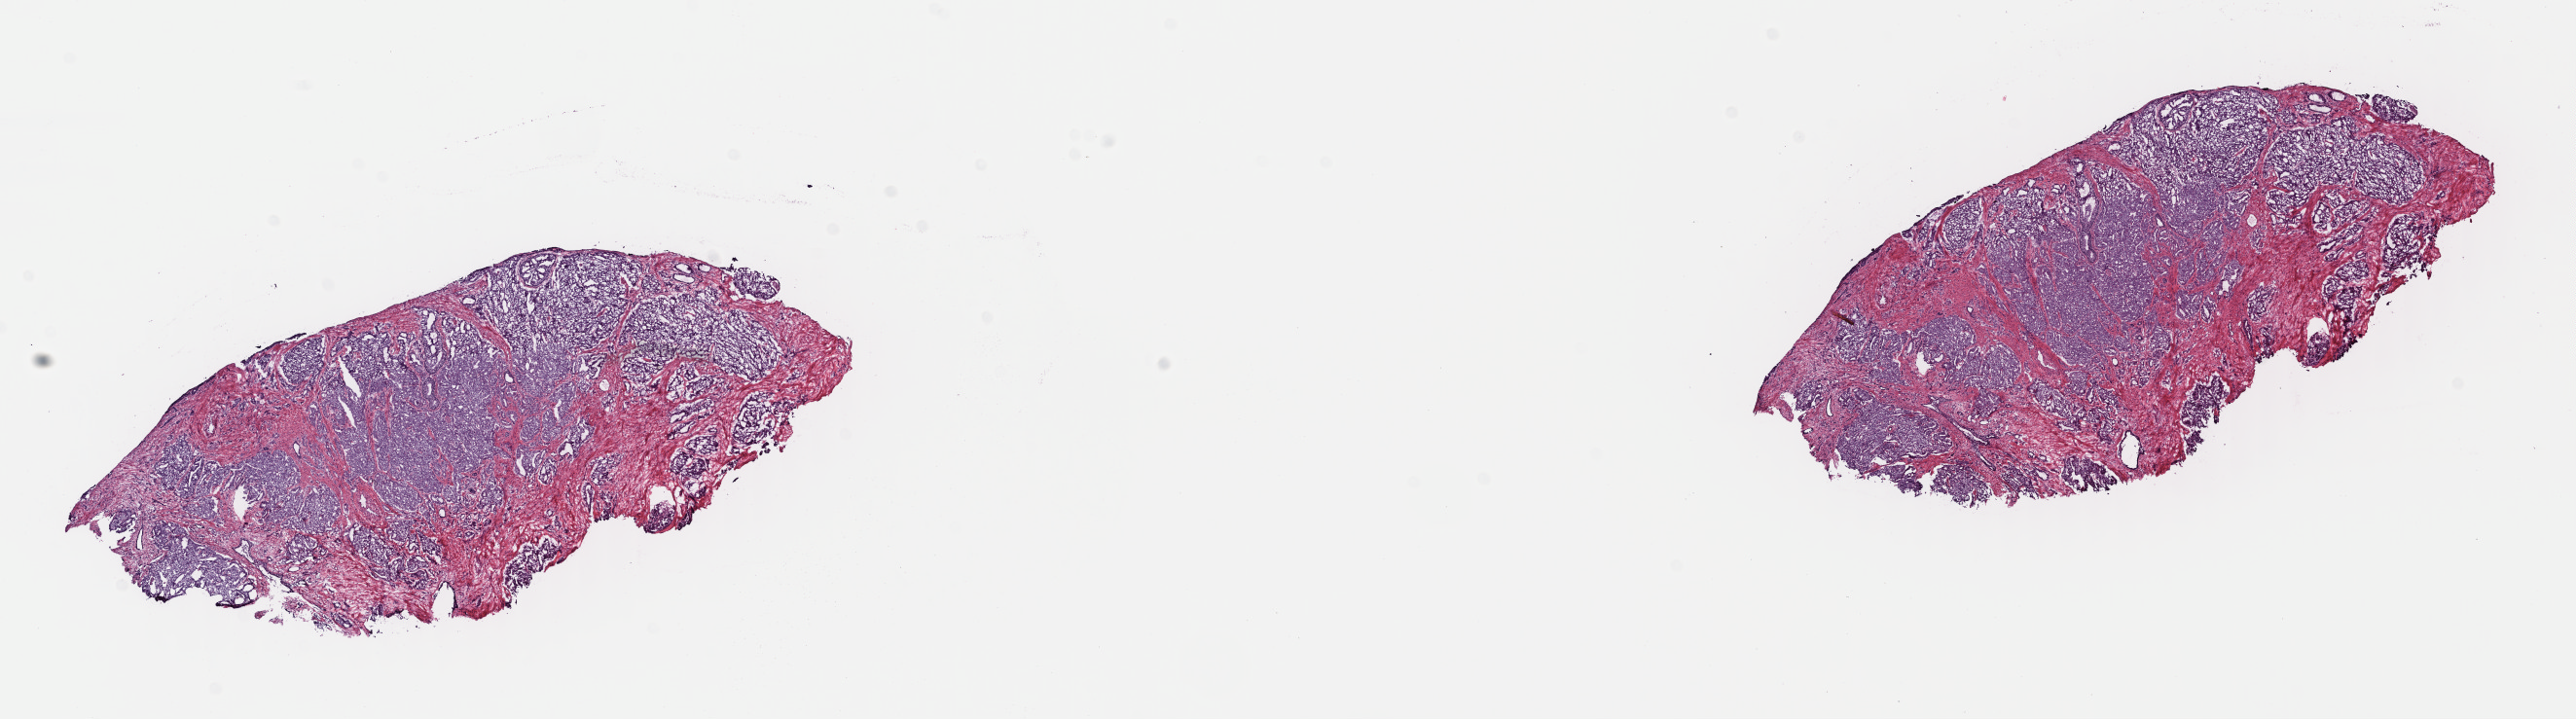
Whole-slide histology image, H&E-stained — shown as a low-resolution overview of the whole scanned area (about 20.8 x 5.8 mm, acquisition: 40x scan); frozen section; primary tumour sample from the prostate. Patient: male, age at initial diagnosis 65 years. Gleason score: 8 (4+4). Slide review estimates, as recorded: tumour cells 80%, tumour nuclei 80%, normal cells 0%, stromal cells 20%, necrosis 0%. Inflammatory infiltration, as recorded: lymphocyte infiltration 40%, monocyte infiltration 20%, neutrophil infiltration 20%.
Laterality: bilateral. Histologic diagnosis: Adenocarcinoma, NOS (prostate gland). Lymph nodes positive (case pathology): 0 of 4 examined.